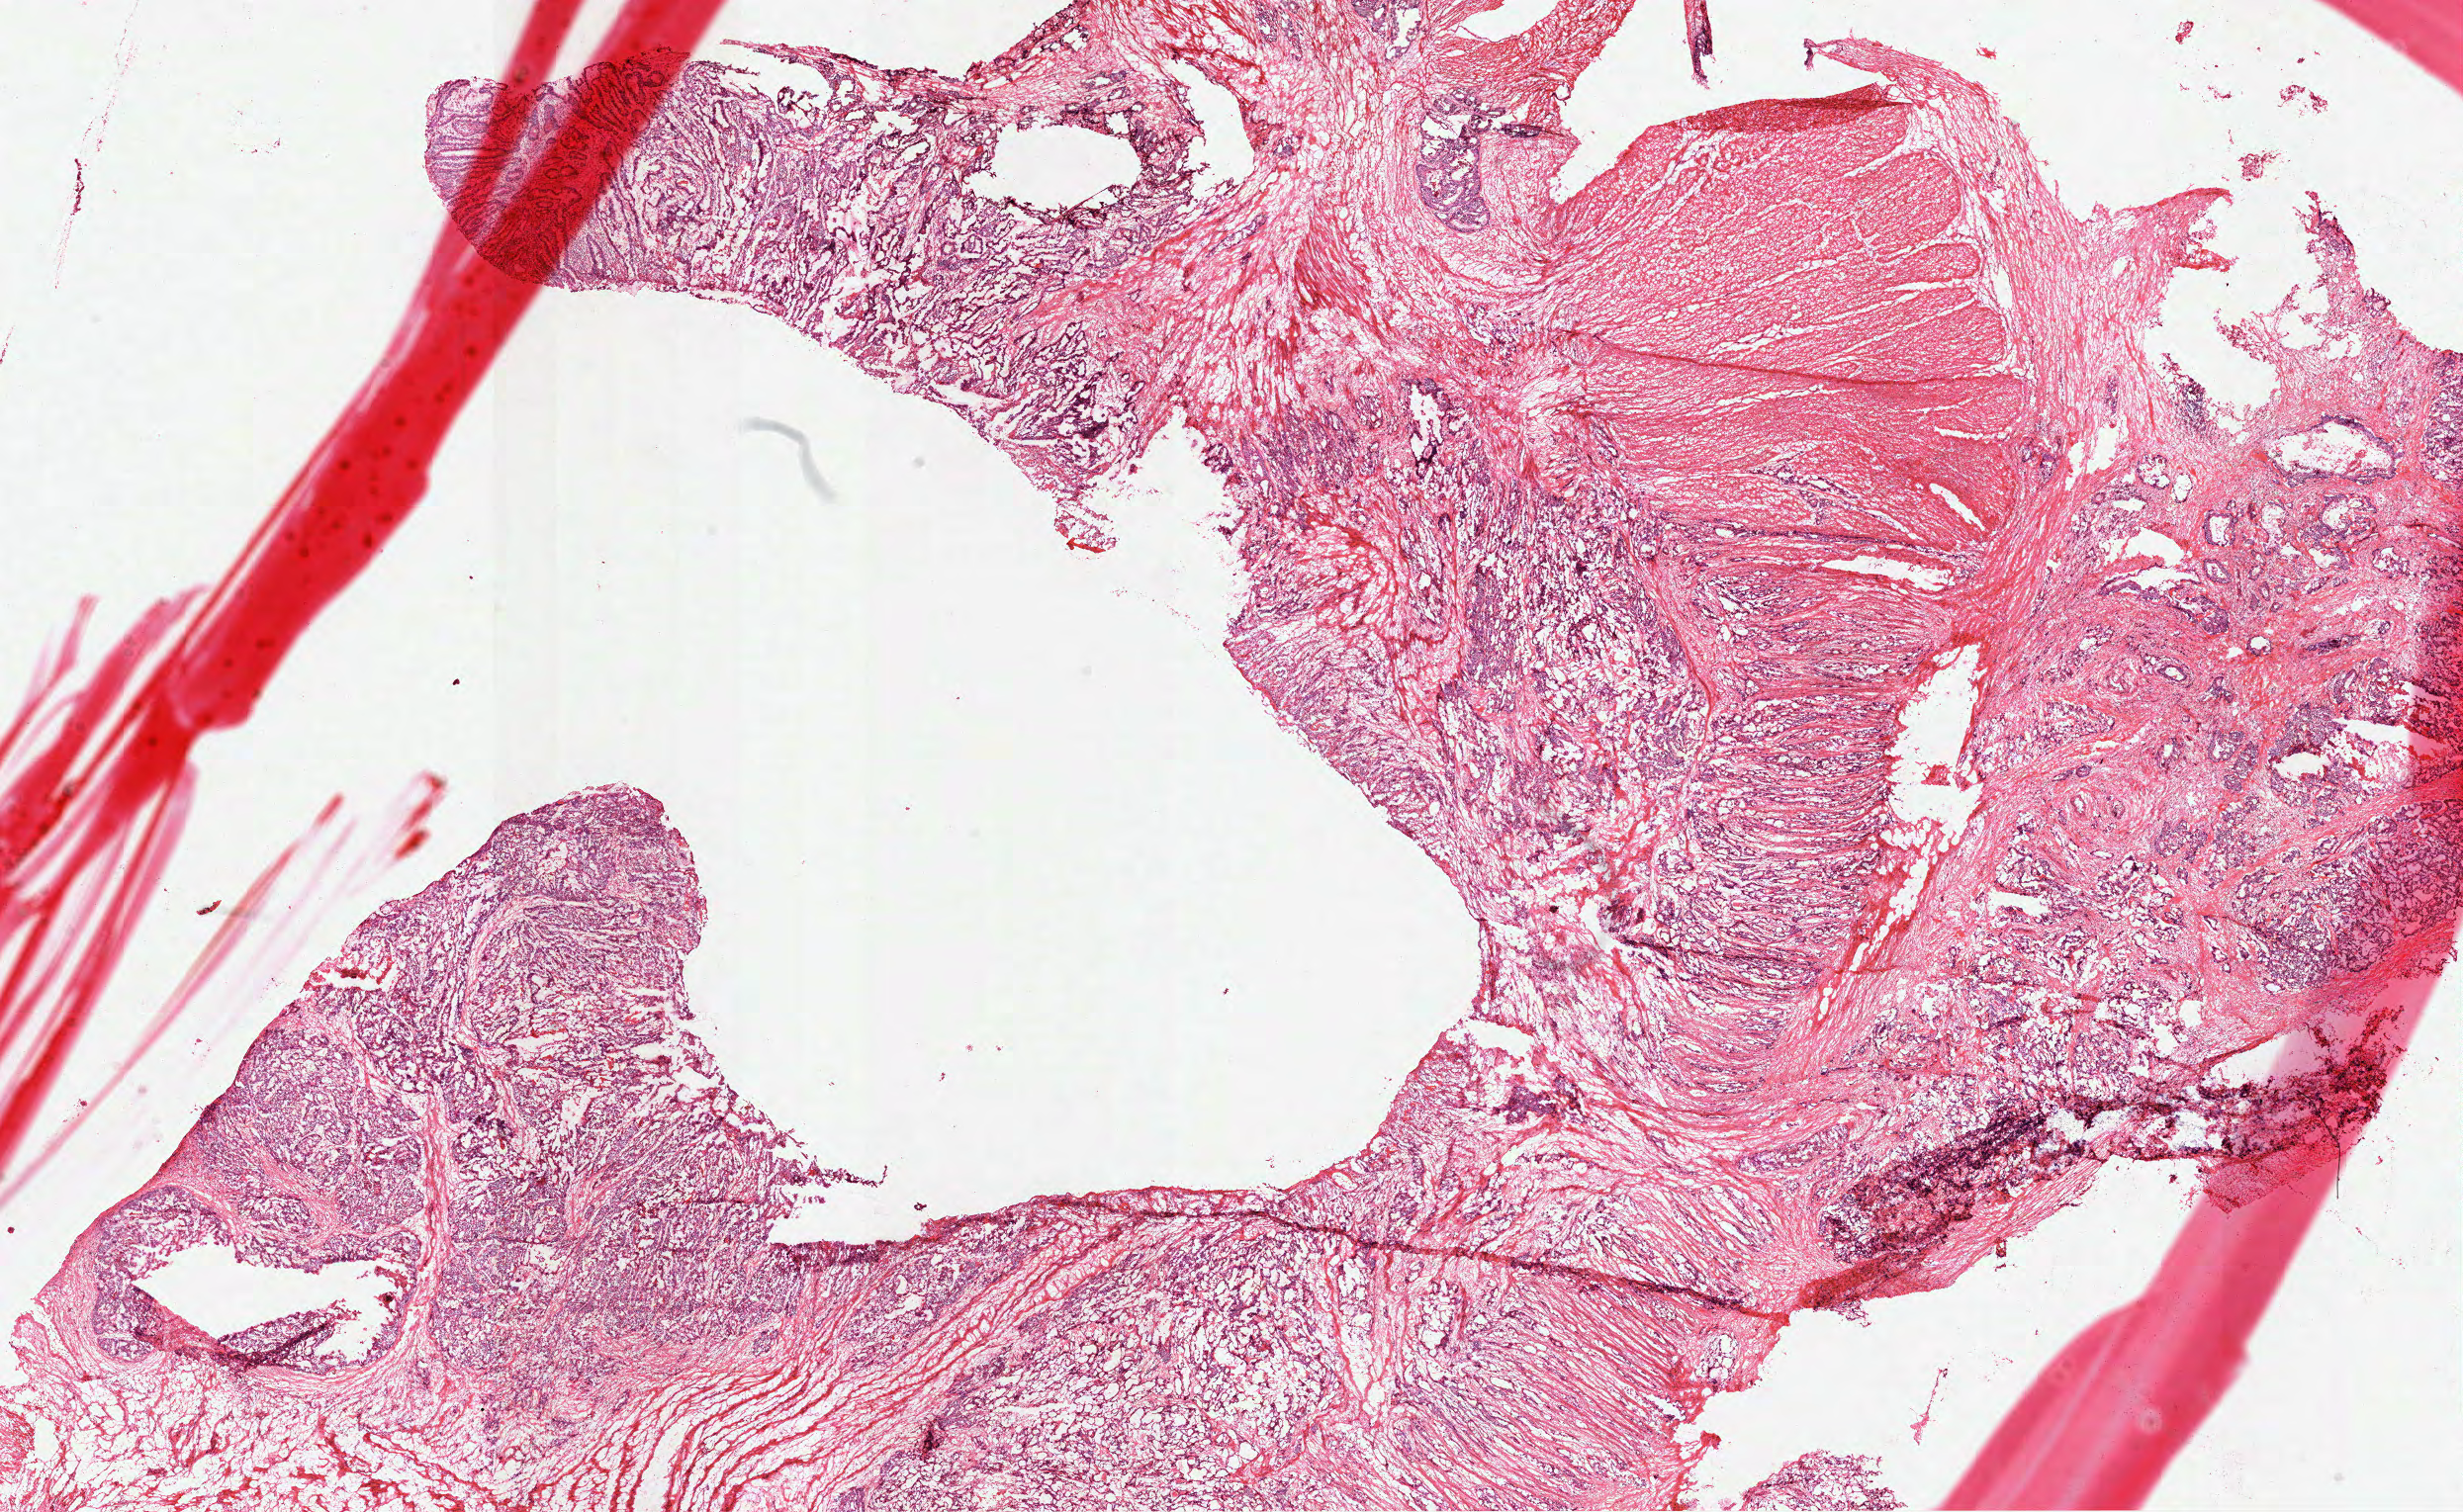
Digitized H&E tissue section (whole slide), whole scanned area (about 20.1 x 12.3 mm) shown as a low-resolution overview; frozen section; sample: primary tumour, colon. Female, age 61 years at initial diagnosis. Composition of this section per pathologist review: tumour cells 87%, tumour nuclei 80%, normal cells 0%, stromal cells 10%, necrosis 3%. Inflammatory infiltration, as recorded: lymphocyte infiltration 5%, monocyte infiltration 0%, neutrophil infiltration 1%.
Histologic diagnosis: Adenocarcinoma, NOS. AJCC pathologic stage: IIIB (7th edition).